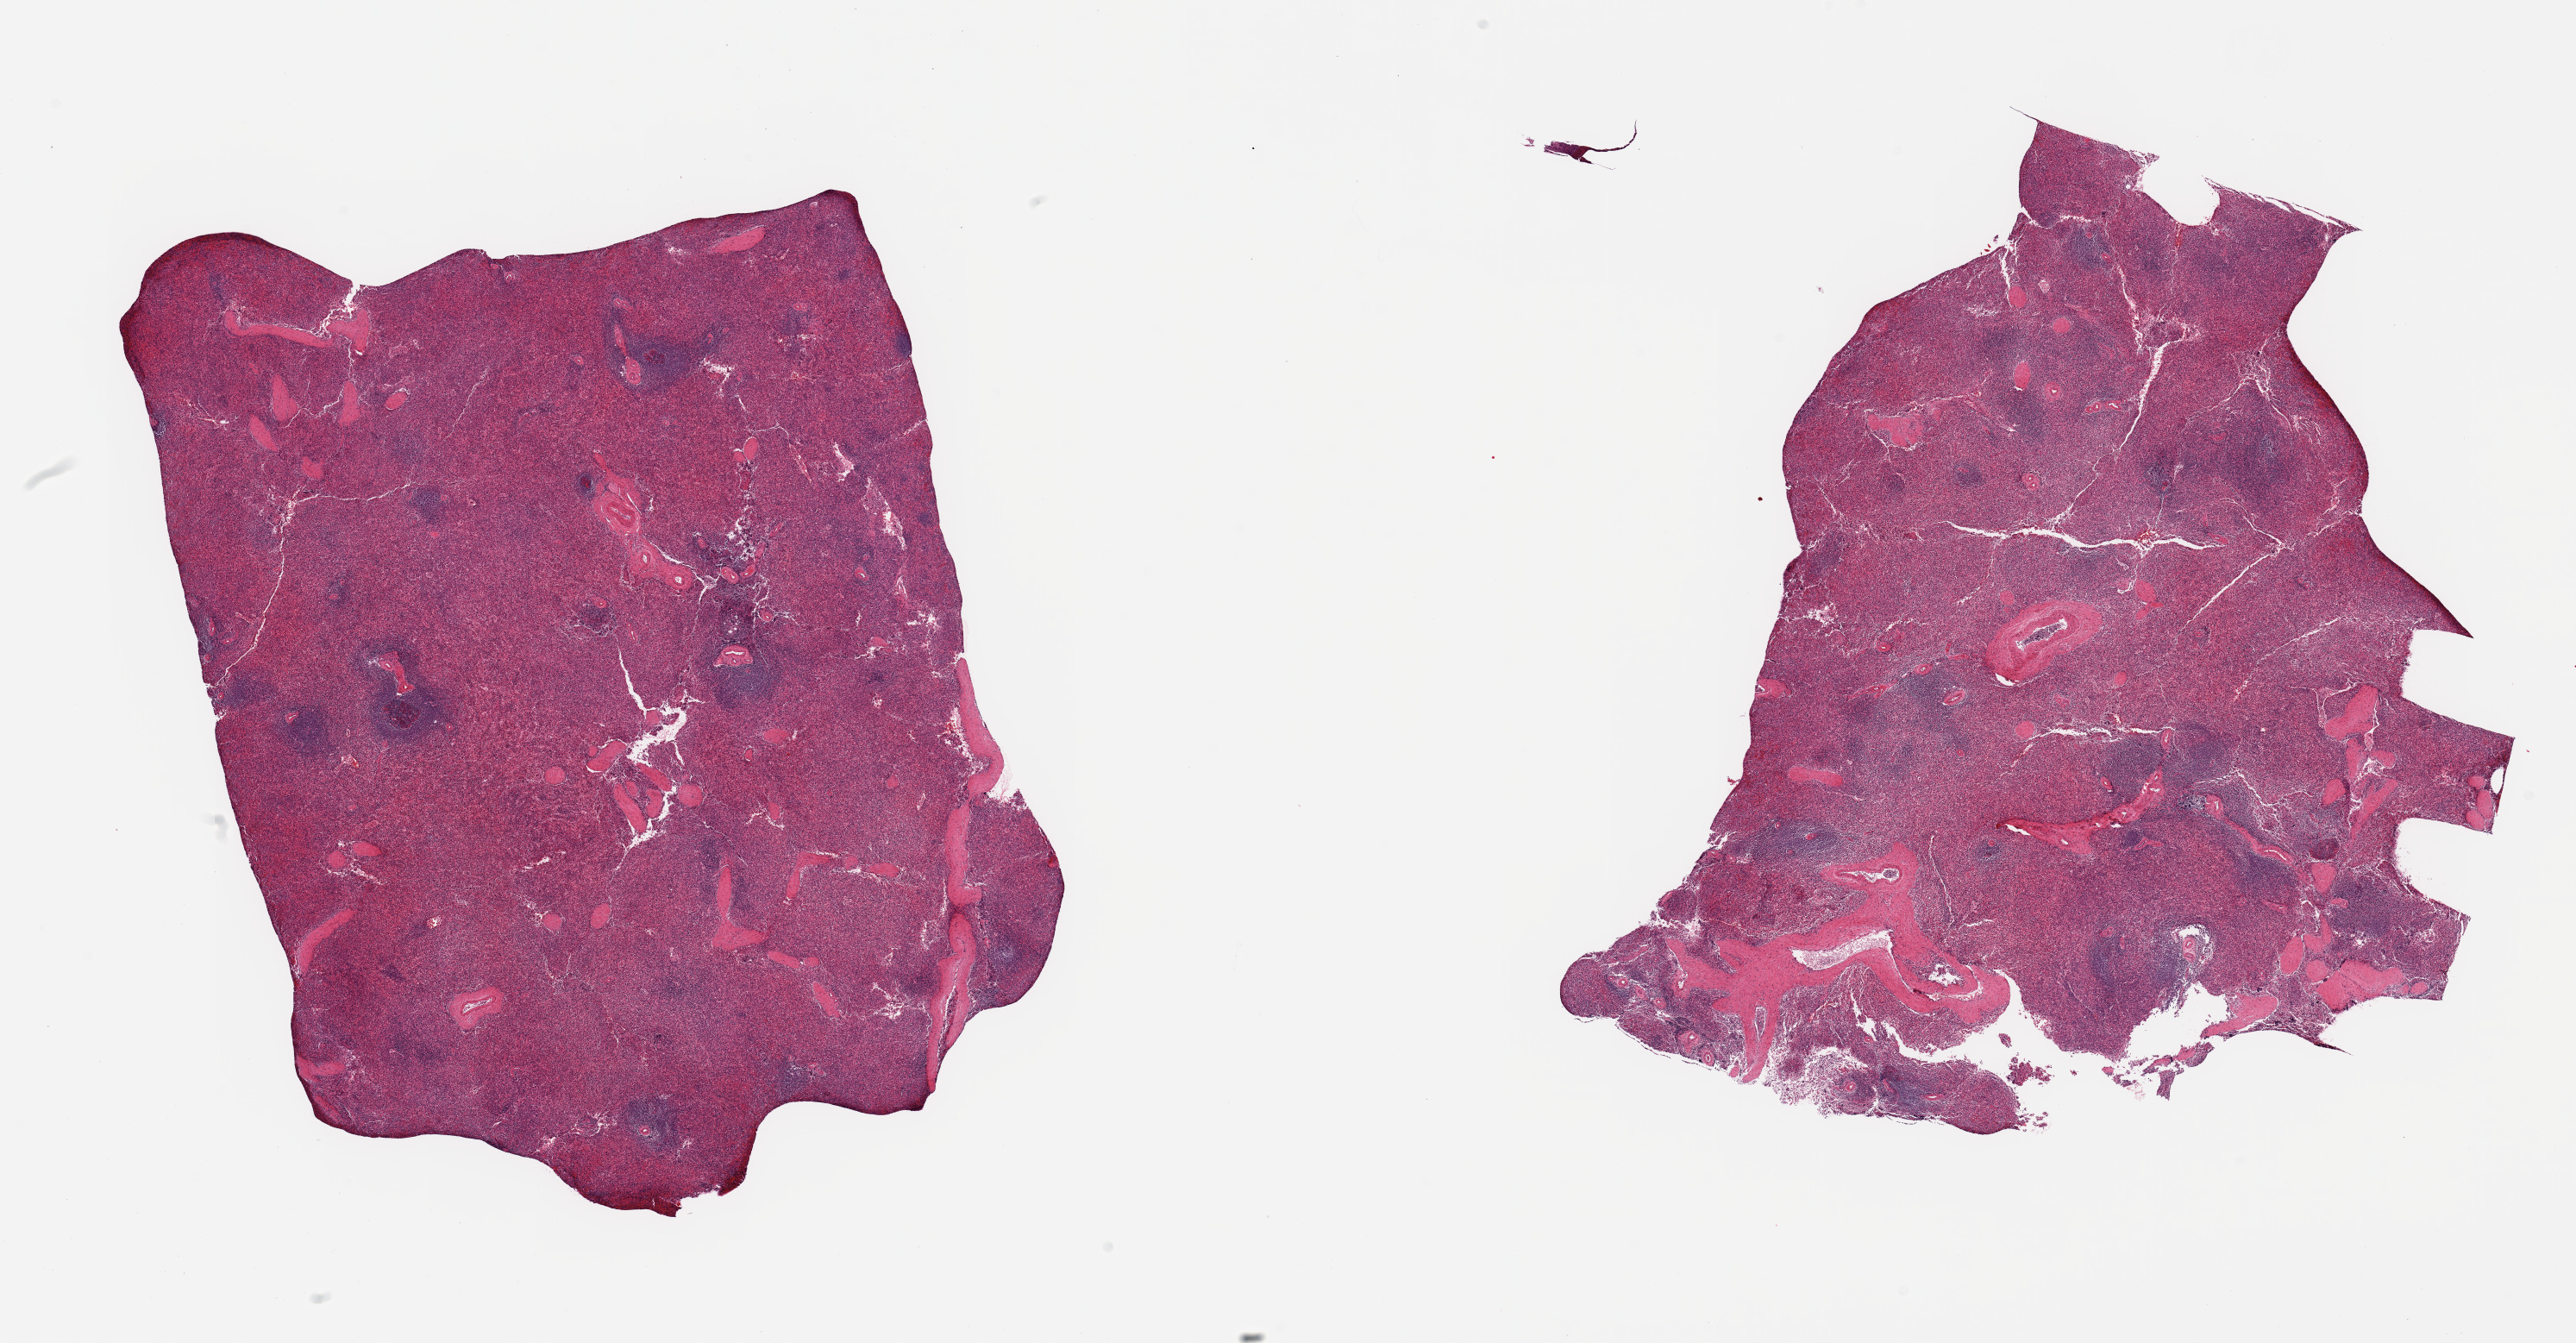
Whole-slide image, haematoxylin and eosin stain, low-resolution overview of the scanned area, about 23.6 x 12.3 mm, PAXgene-fixed, paraffin-embedded tissue, section of spleen (target tissue), tissue donor sample.
Review note (as recorded): 2 pieces, no abnormalities.